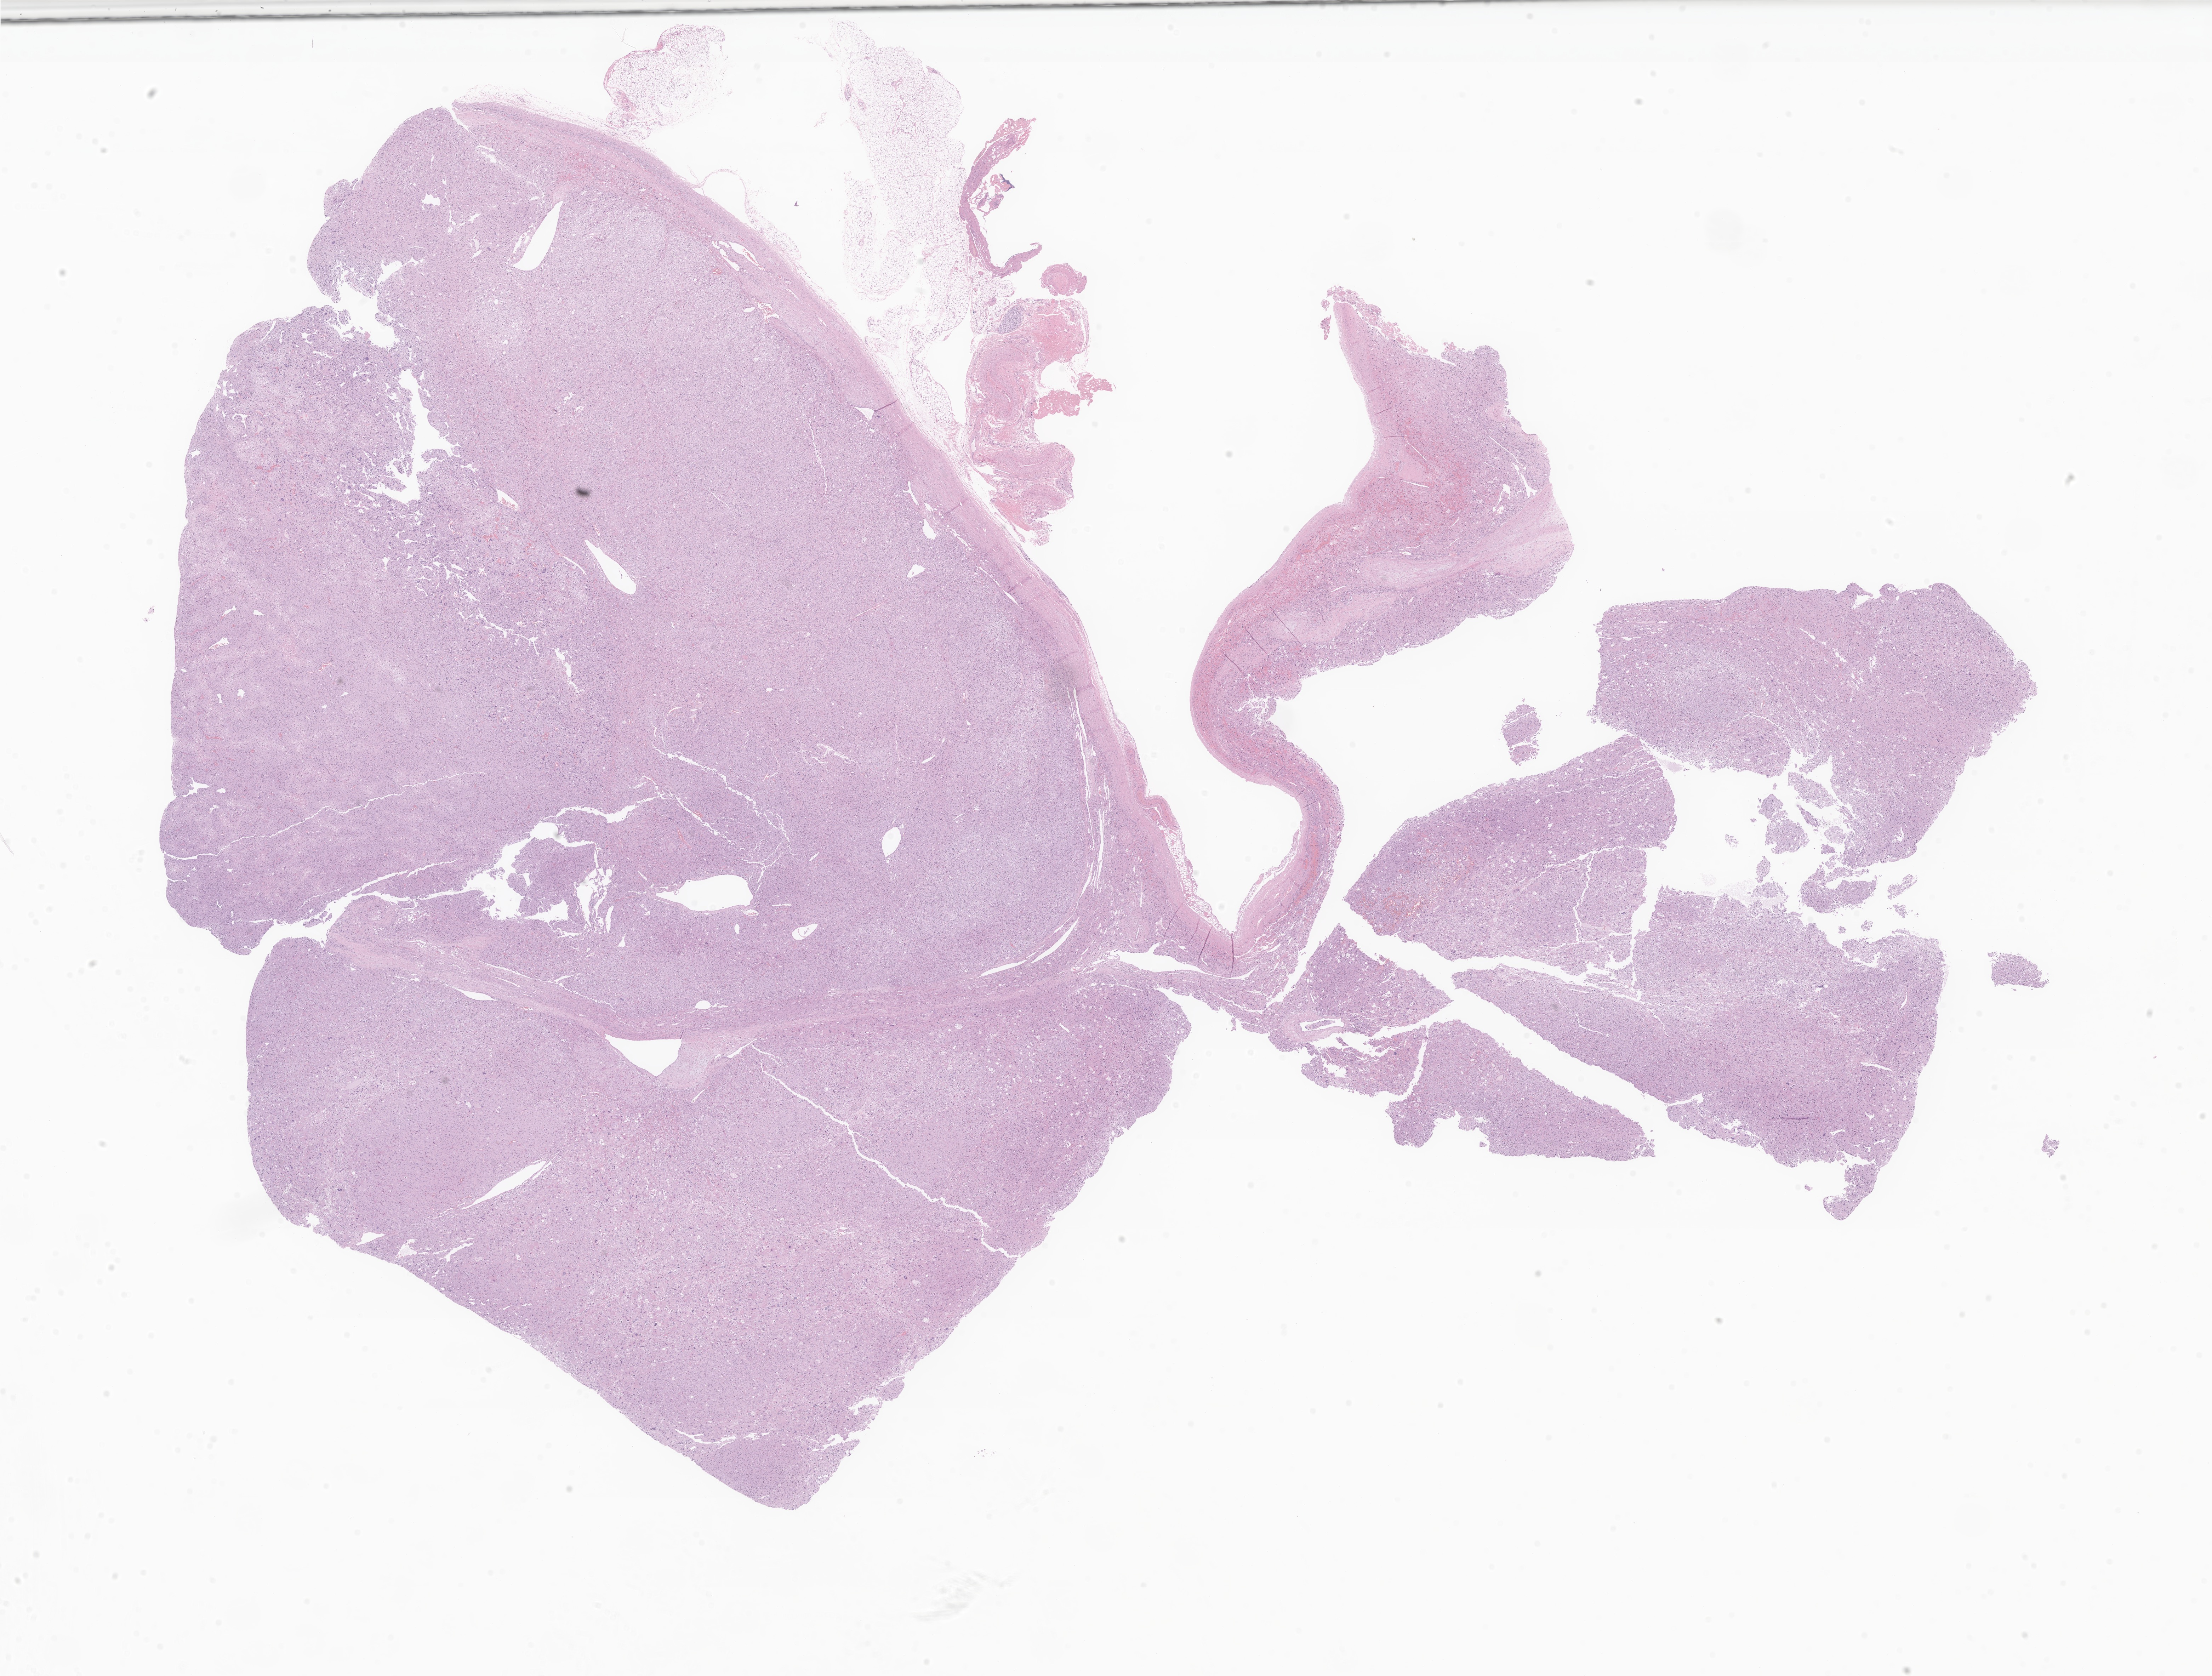
Digitized H&E-stained section of tumor tissue from the adrenal gland, low-resolution overview of the scanned area, about 26.3 x 20.0 mm. Formalin-fixed paraffin-embedded section. Female patient, age 38 months (3 years 2 months).
Diagnosis (ICD-O-3 morphology term): Adrenal cortical carcinoma.